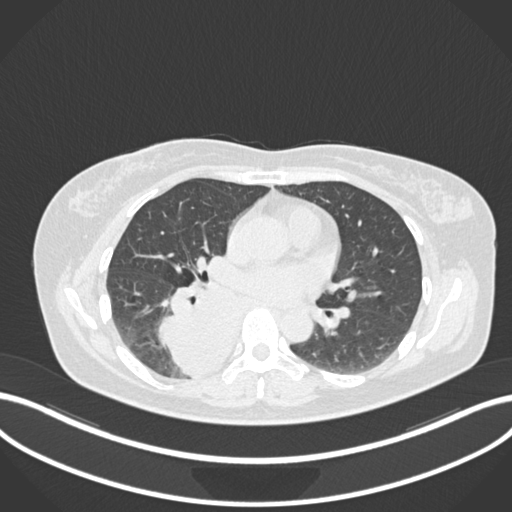
Chest CT, one axial slice. Slice 587 of 677 in the series (ordered by position). Reconstruction kernel B30f. Lung window (W 1500 / L -600 HU). 512 × 512 image matrix. Patient: female, 54 years. Case-level facts recorded for this patient, not image findings: clinical TNM (as recorded): T4 N0 M0.
Annotated regions visible in this slice (bounding box drawn by a radiologist):
- lung tumour (recorded histology: adenocarcinoma): bounding box (x1, y1, x2, y2) in pixels: (155, 273, 238, 386)